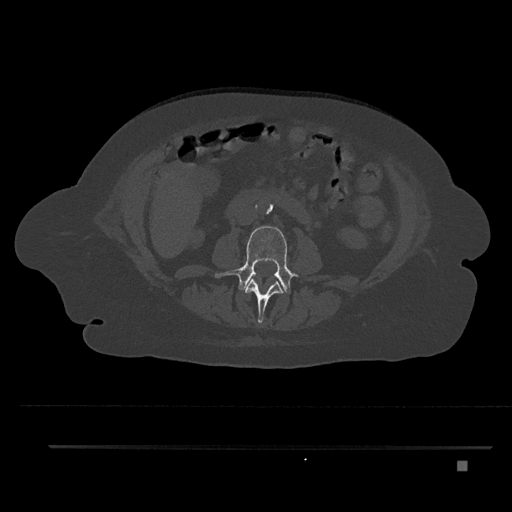
CT including the spine, one axial slice. Position 143 of 797 along the scan axis. 120 kVp. Bone window (W 1800 / L 400 HU). 0.5 mm slice thickness. 512 × 512 image matrix. Patient: female, 76 years. From the clinical record (not read from this slice): primary cancer: lung; vertebrae with lytic lesions (as recorded): T11, L3.
Annotated regions visible in this slice (semi-automatically segmented with operator editing):
- L2 vertebra: bounding box <245,278,284,324> (left, top, right, bottom; pixels)
- L3 vertebra: <215,226,294,295>